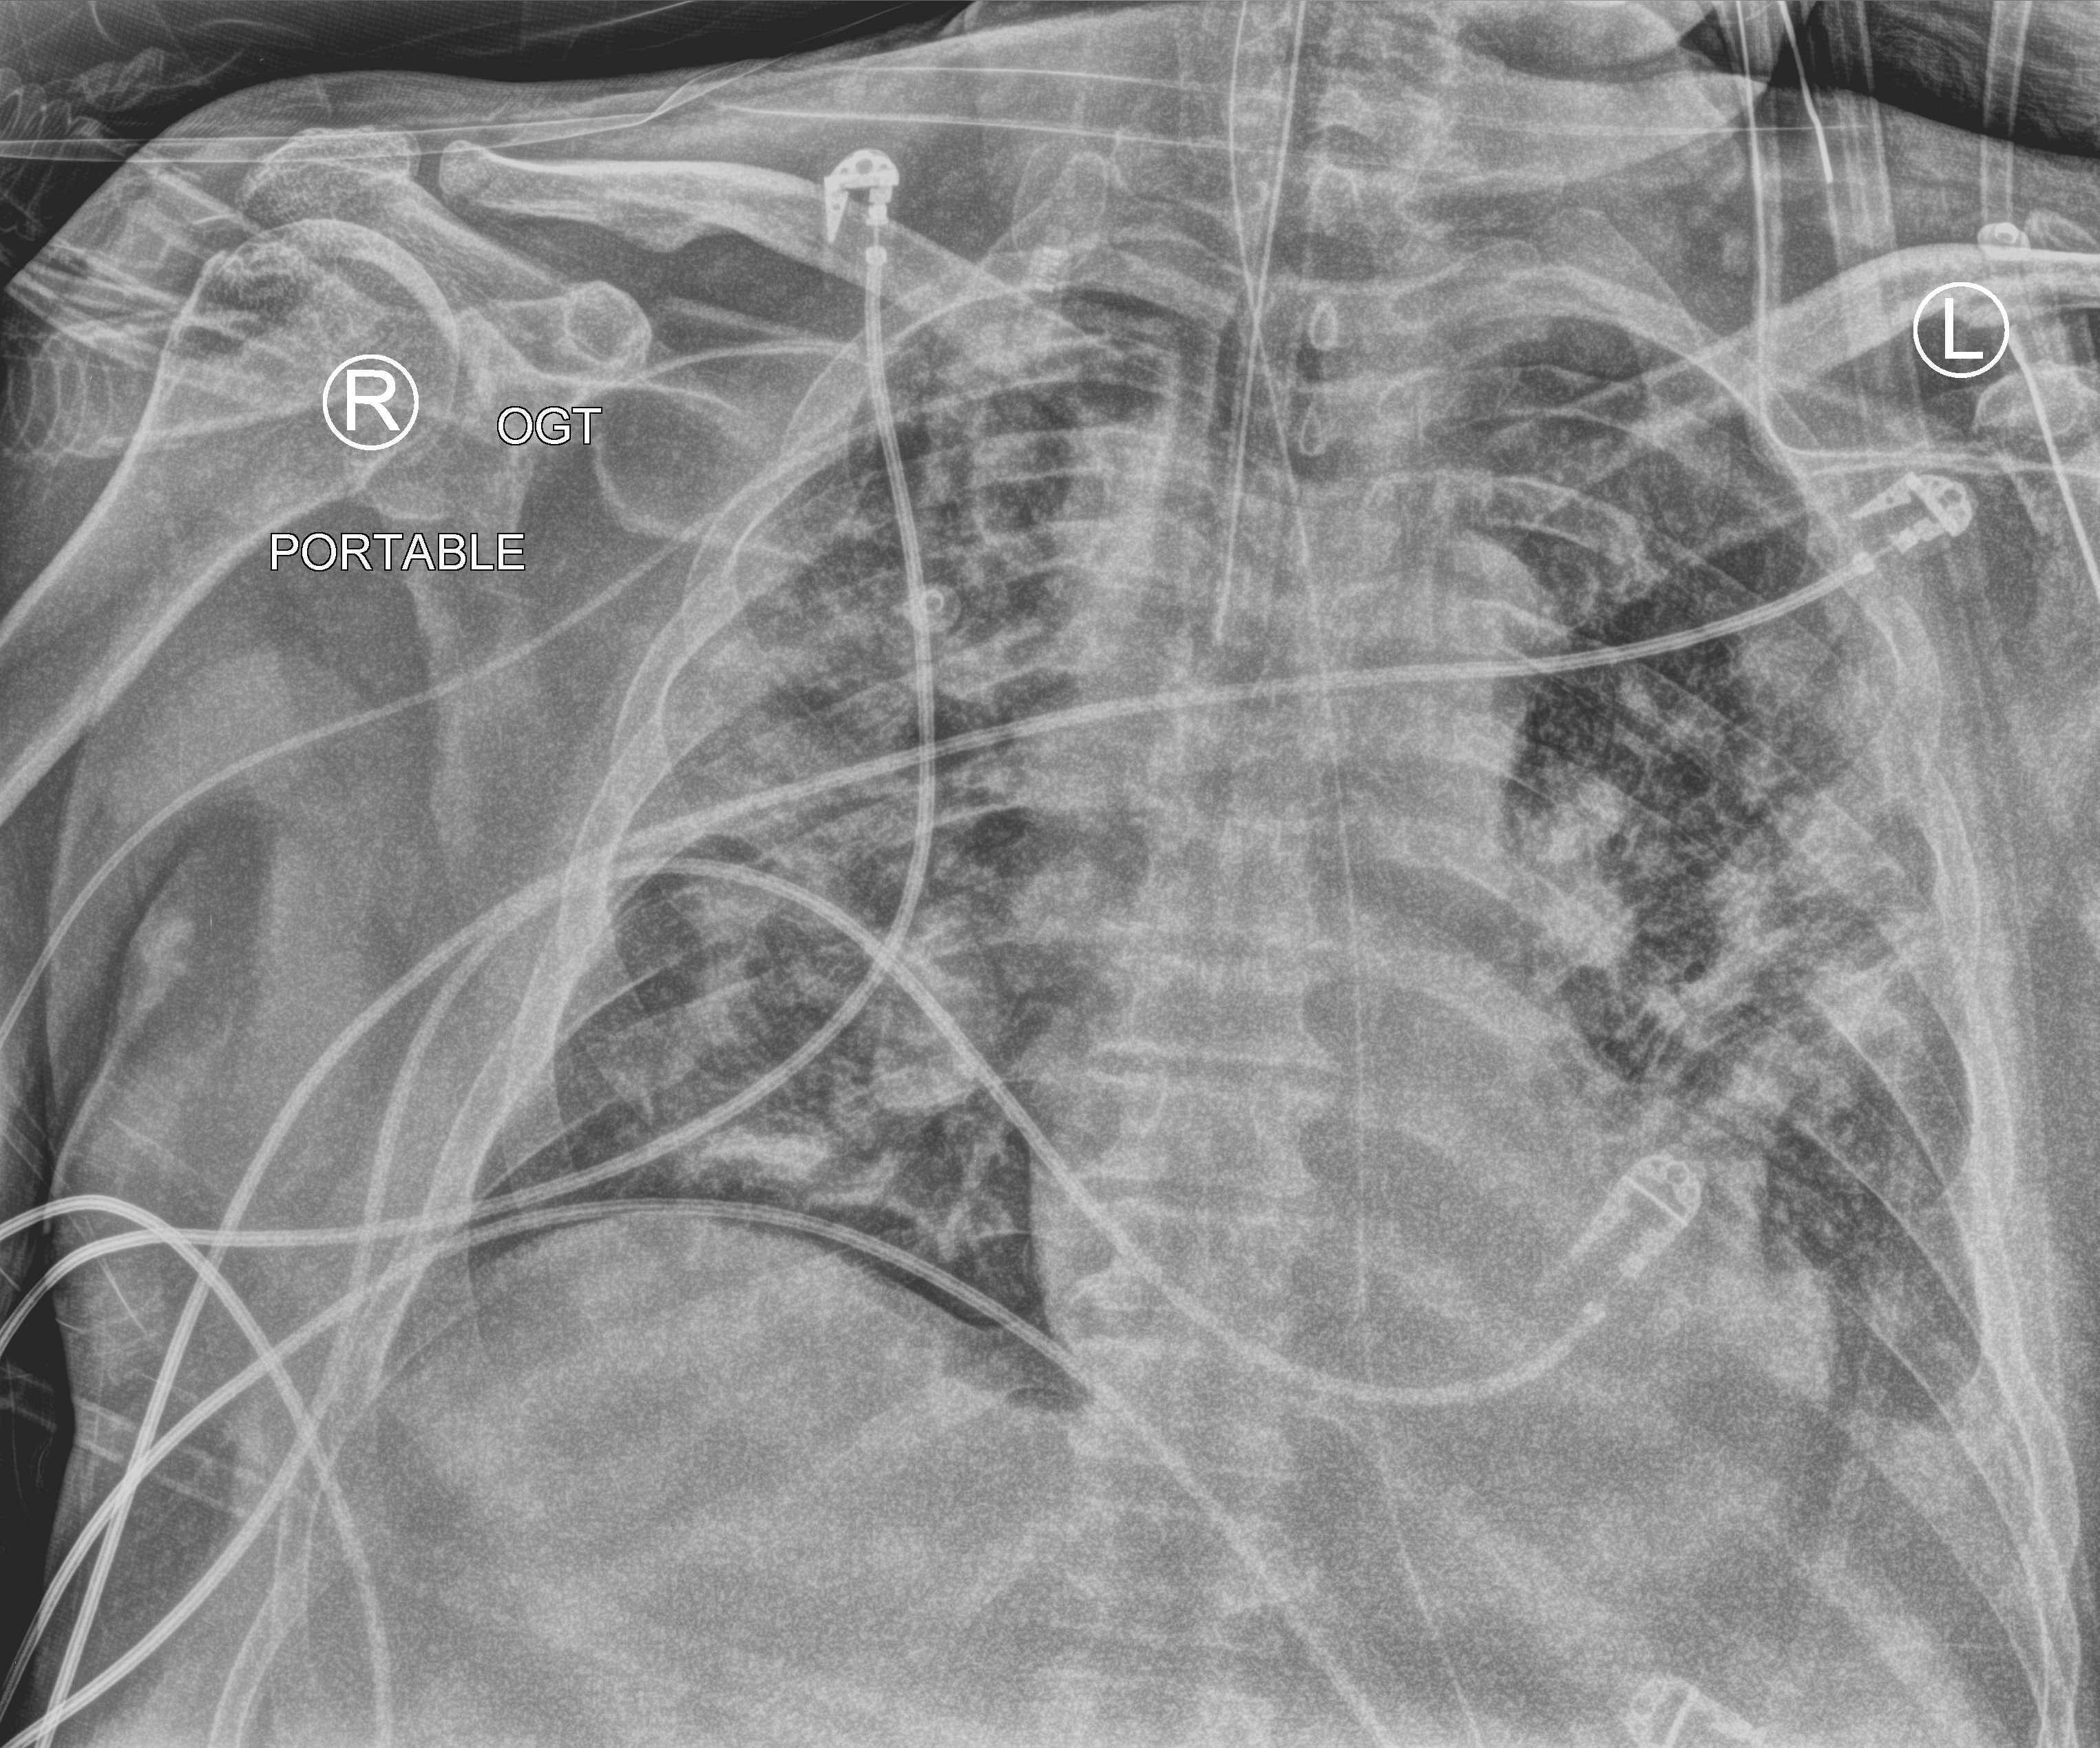
Portable chest radiograph, anteroposterior (AP) projection. Patient hospitalised with COVID-19; male, aged 60–74 years.
Hospital-stay facts (about this admission, not read from this image; timing relative to this image not recorded):
- length of hospital stay: 24 days